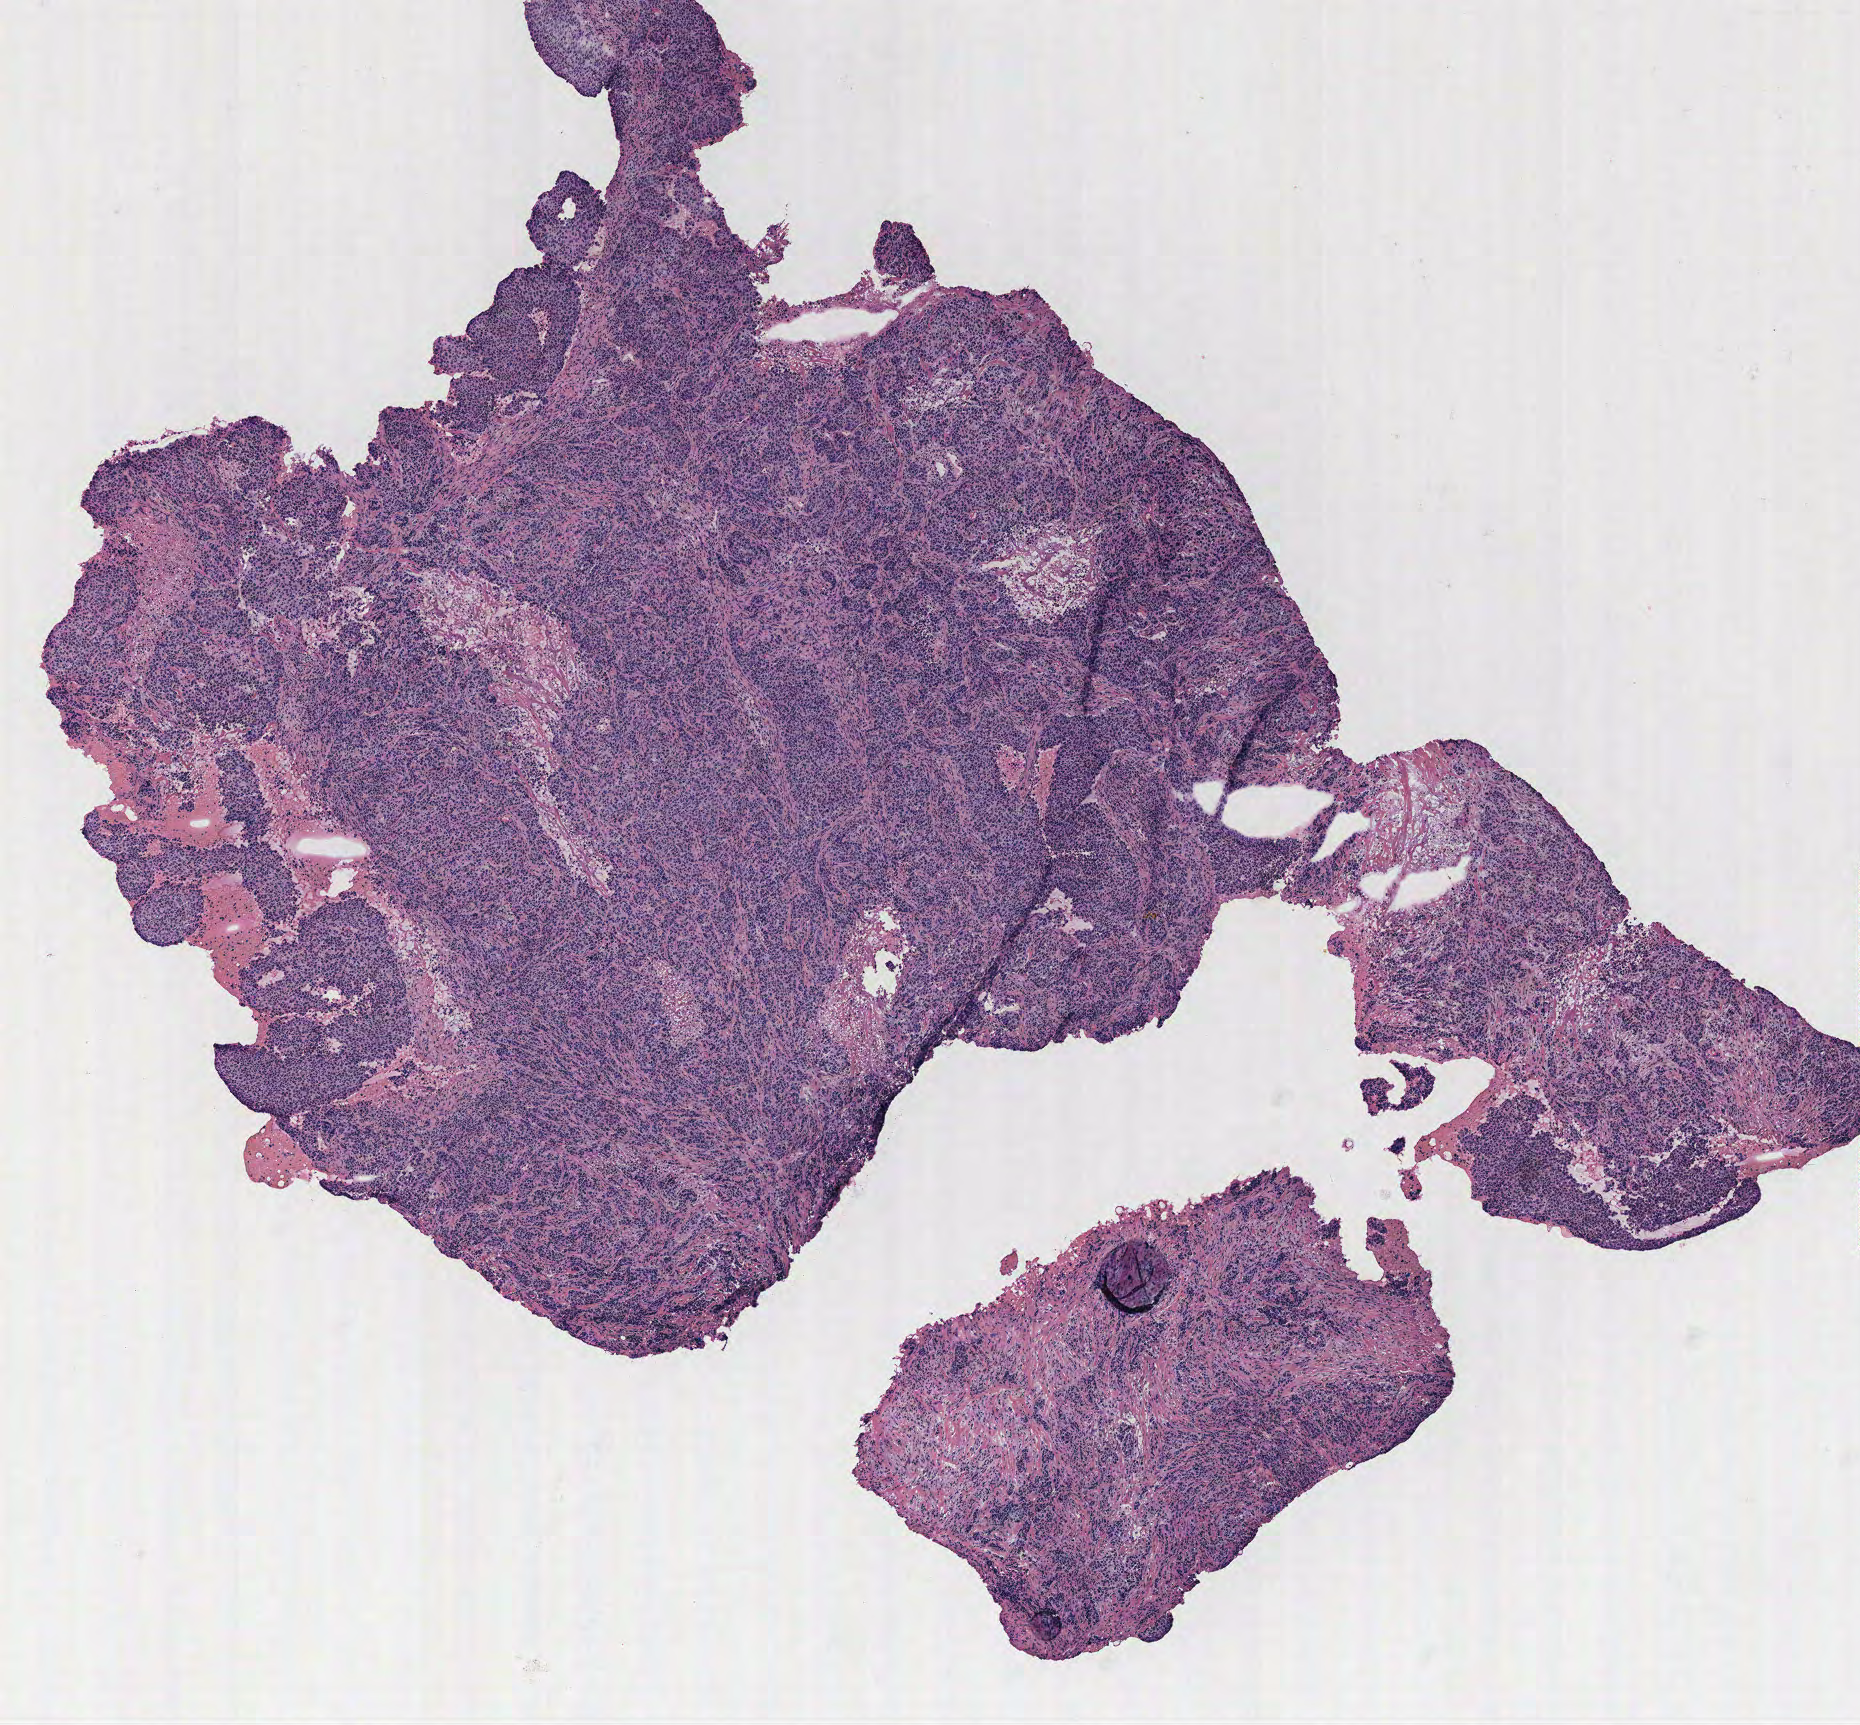
Digitized H&E-stained tissue section (whole slide) — whole scanned area (about 7.4 x 6.9 mm, slide scanned at 40x) shown as a low-resolution overview, tumour tissue sample, breast. 55-year-old female patient.
Histologic diagnosis: Infiltrating duct carcinoma, NOS. AJCC pathologic stage: IIA.